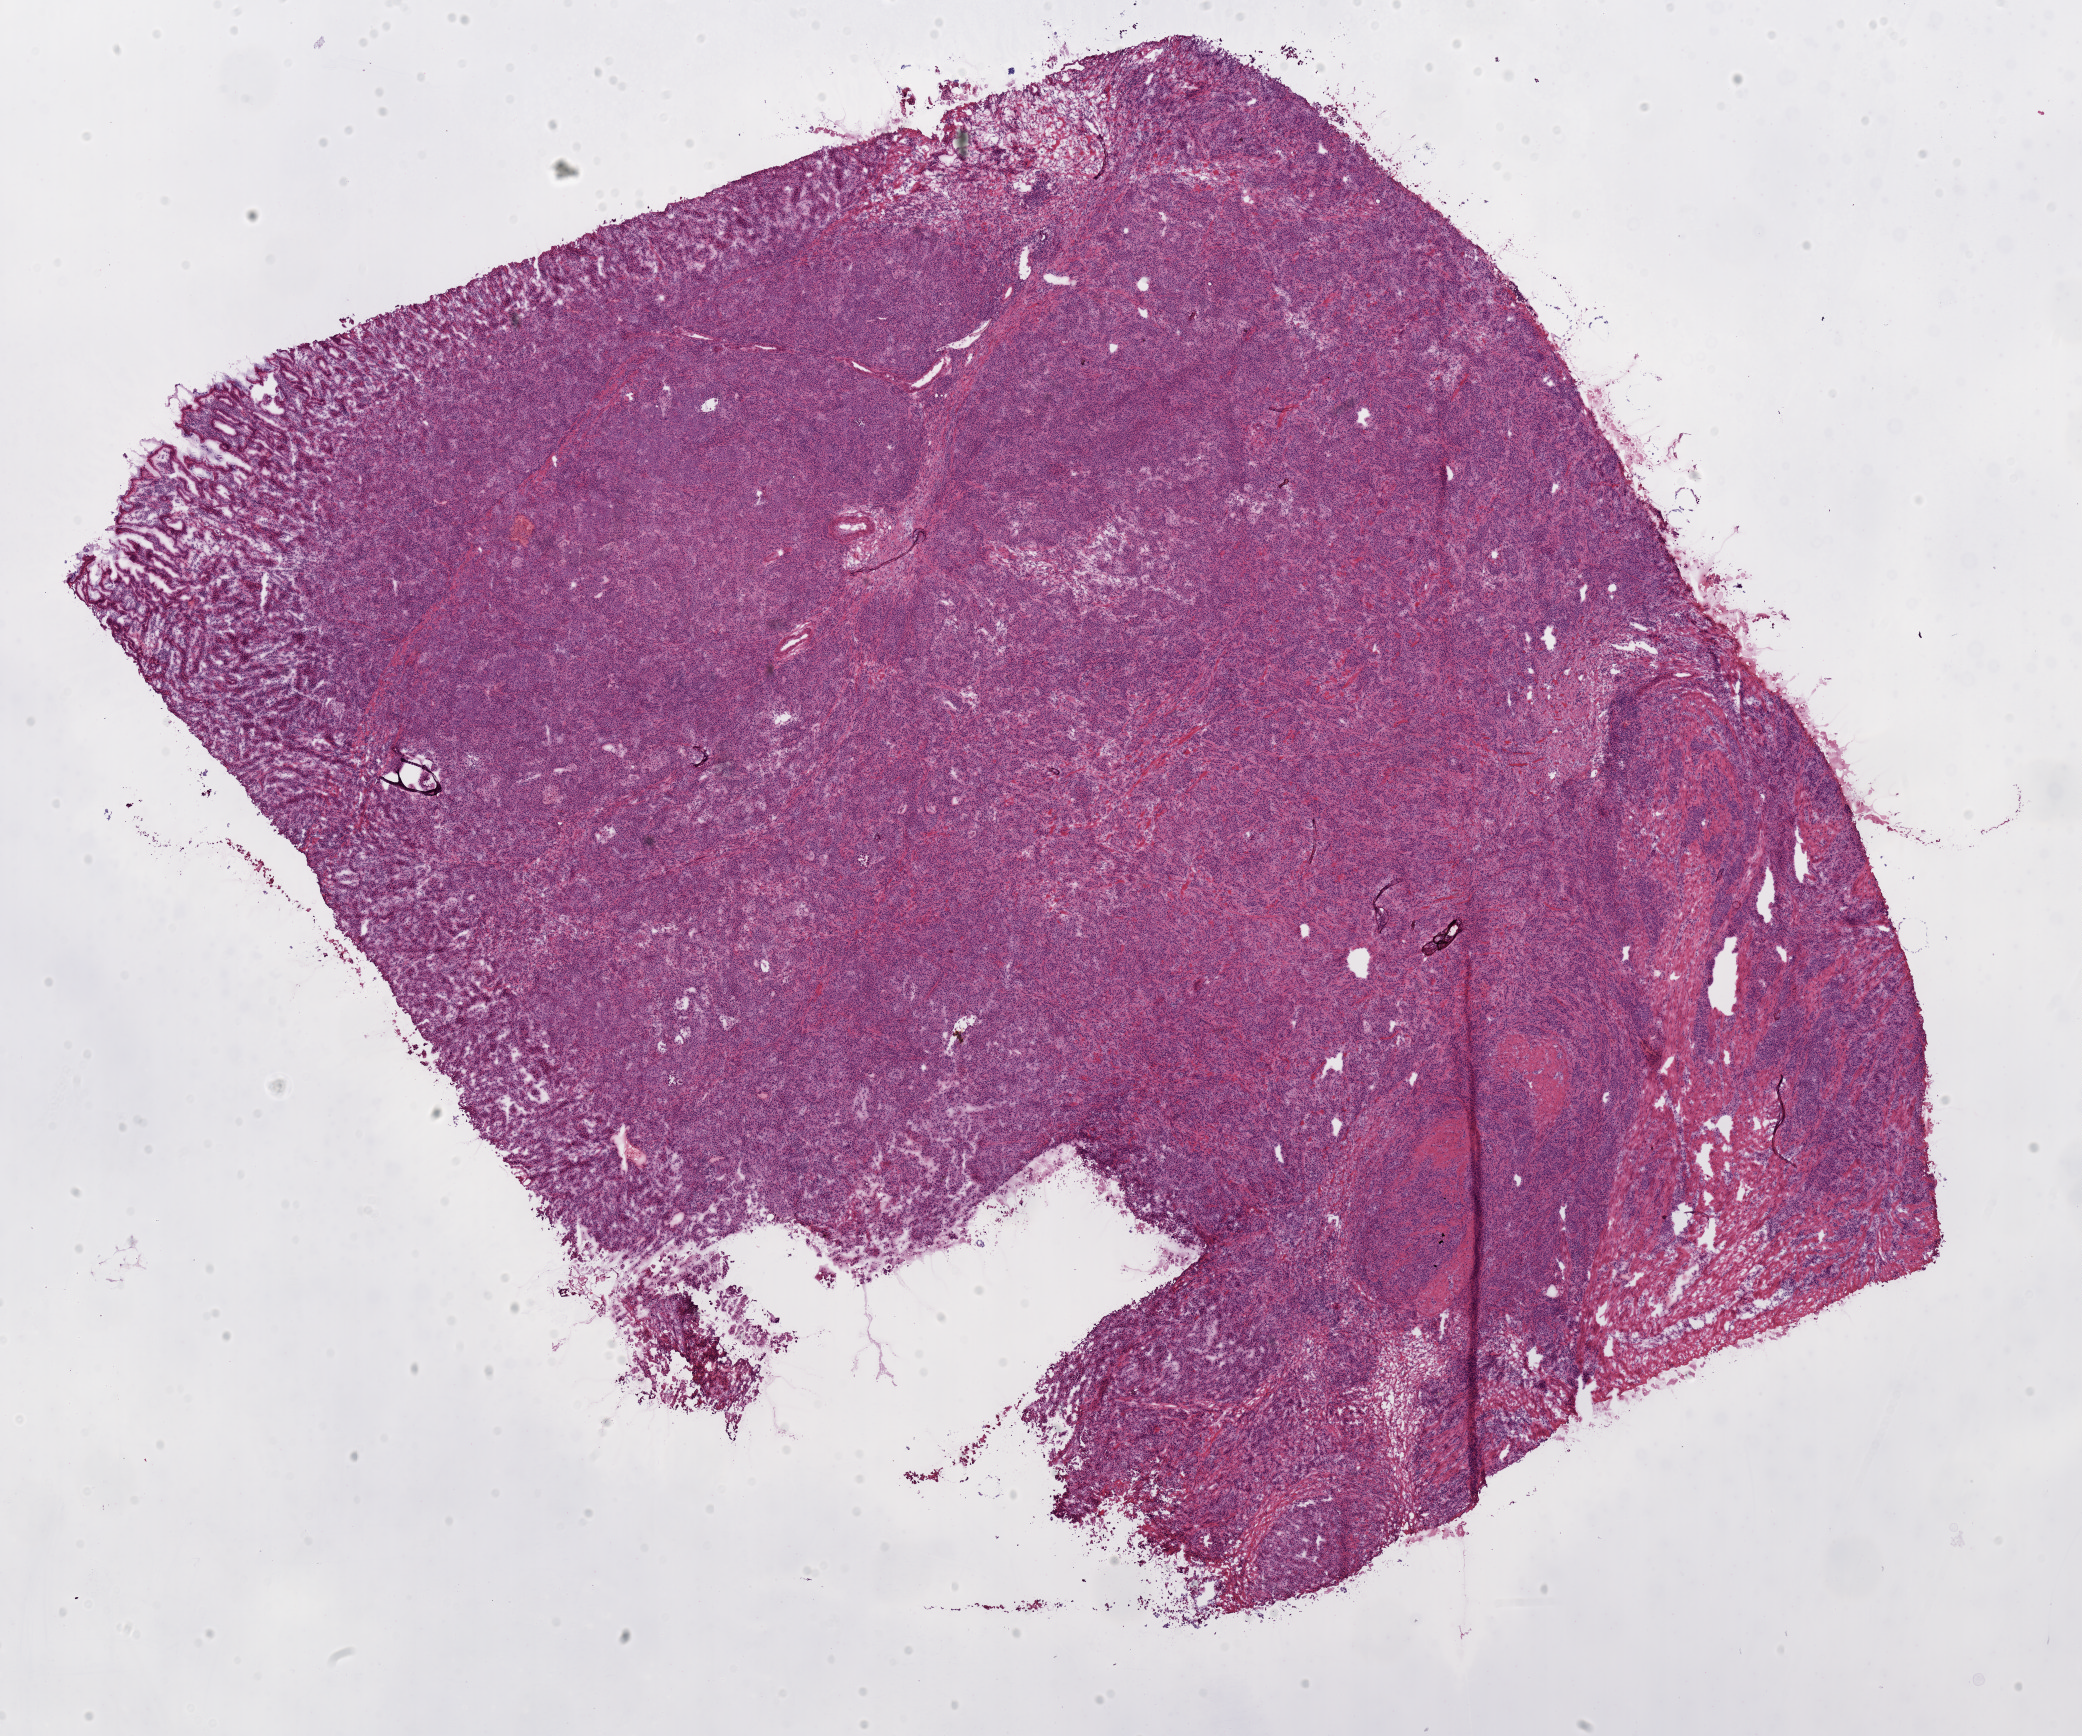
Whole-slide histology image, H&E, whole scanned area (about 16.5 x 13.8 mm, from a 20x scan) shown as a low-resolution overview; frozen section from the top of the tissue portion; sample: primary tumour, stomach. Male, age 69 years at initial diagnosis. Histologic grade: G3 (poorly differentiated). Pathologist review of this section (percent, as recorded): tumour cells 90%, tumour nuclei 80%, normal cells 0%, stromal cells 10%, necrosis 0%.
• TNM: T3 N1 M0
• AJCC pathologic stage: IIIA (6th edition)
• diagnosis: Adenocarcinoma, NOS (gastric antrum)